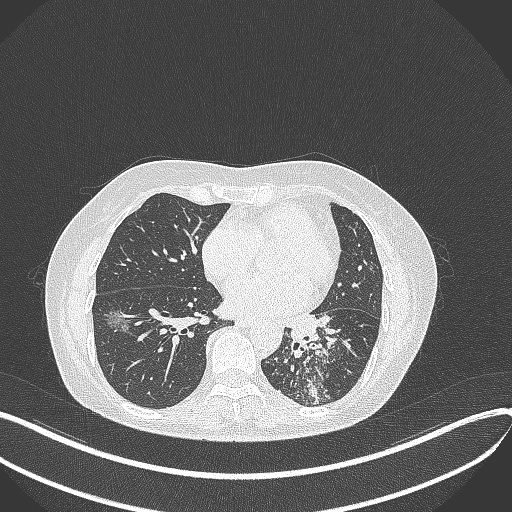
Chest CT, one axial slice. Position 168 of 429 along the scan axis. Reconstruction kernel B70f. 100 kVp. Lung window (W 1500 / L -600 HU). 1 mm slice thickness. 512 × 512 image matrix. Female patient, age 63 years. Case-level facts recorded for this patient, not image findings: clinical TNM (as recorded): T1b N0 M0; histopathological grade: G2-3.
Annotated regions visible in this slice (bounding box drawn by a radiologist):
- lung tumour (recorded histology: adenocarcinoma): bounding box (x1, y1, x2, y2) in pixels: (285, 308, 341, 354)